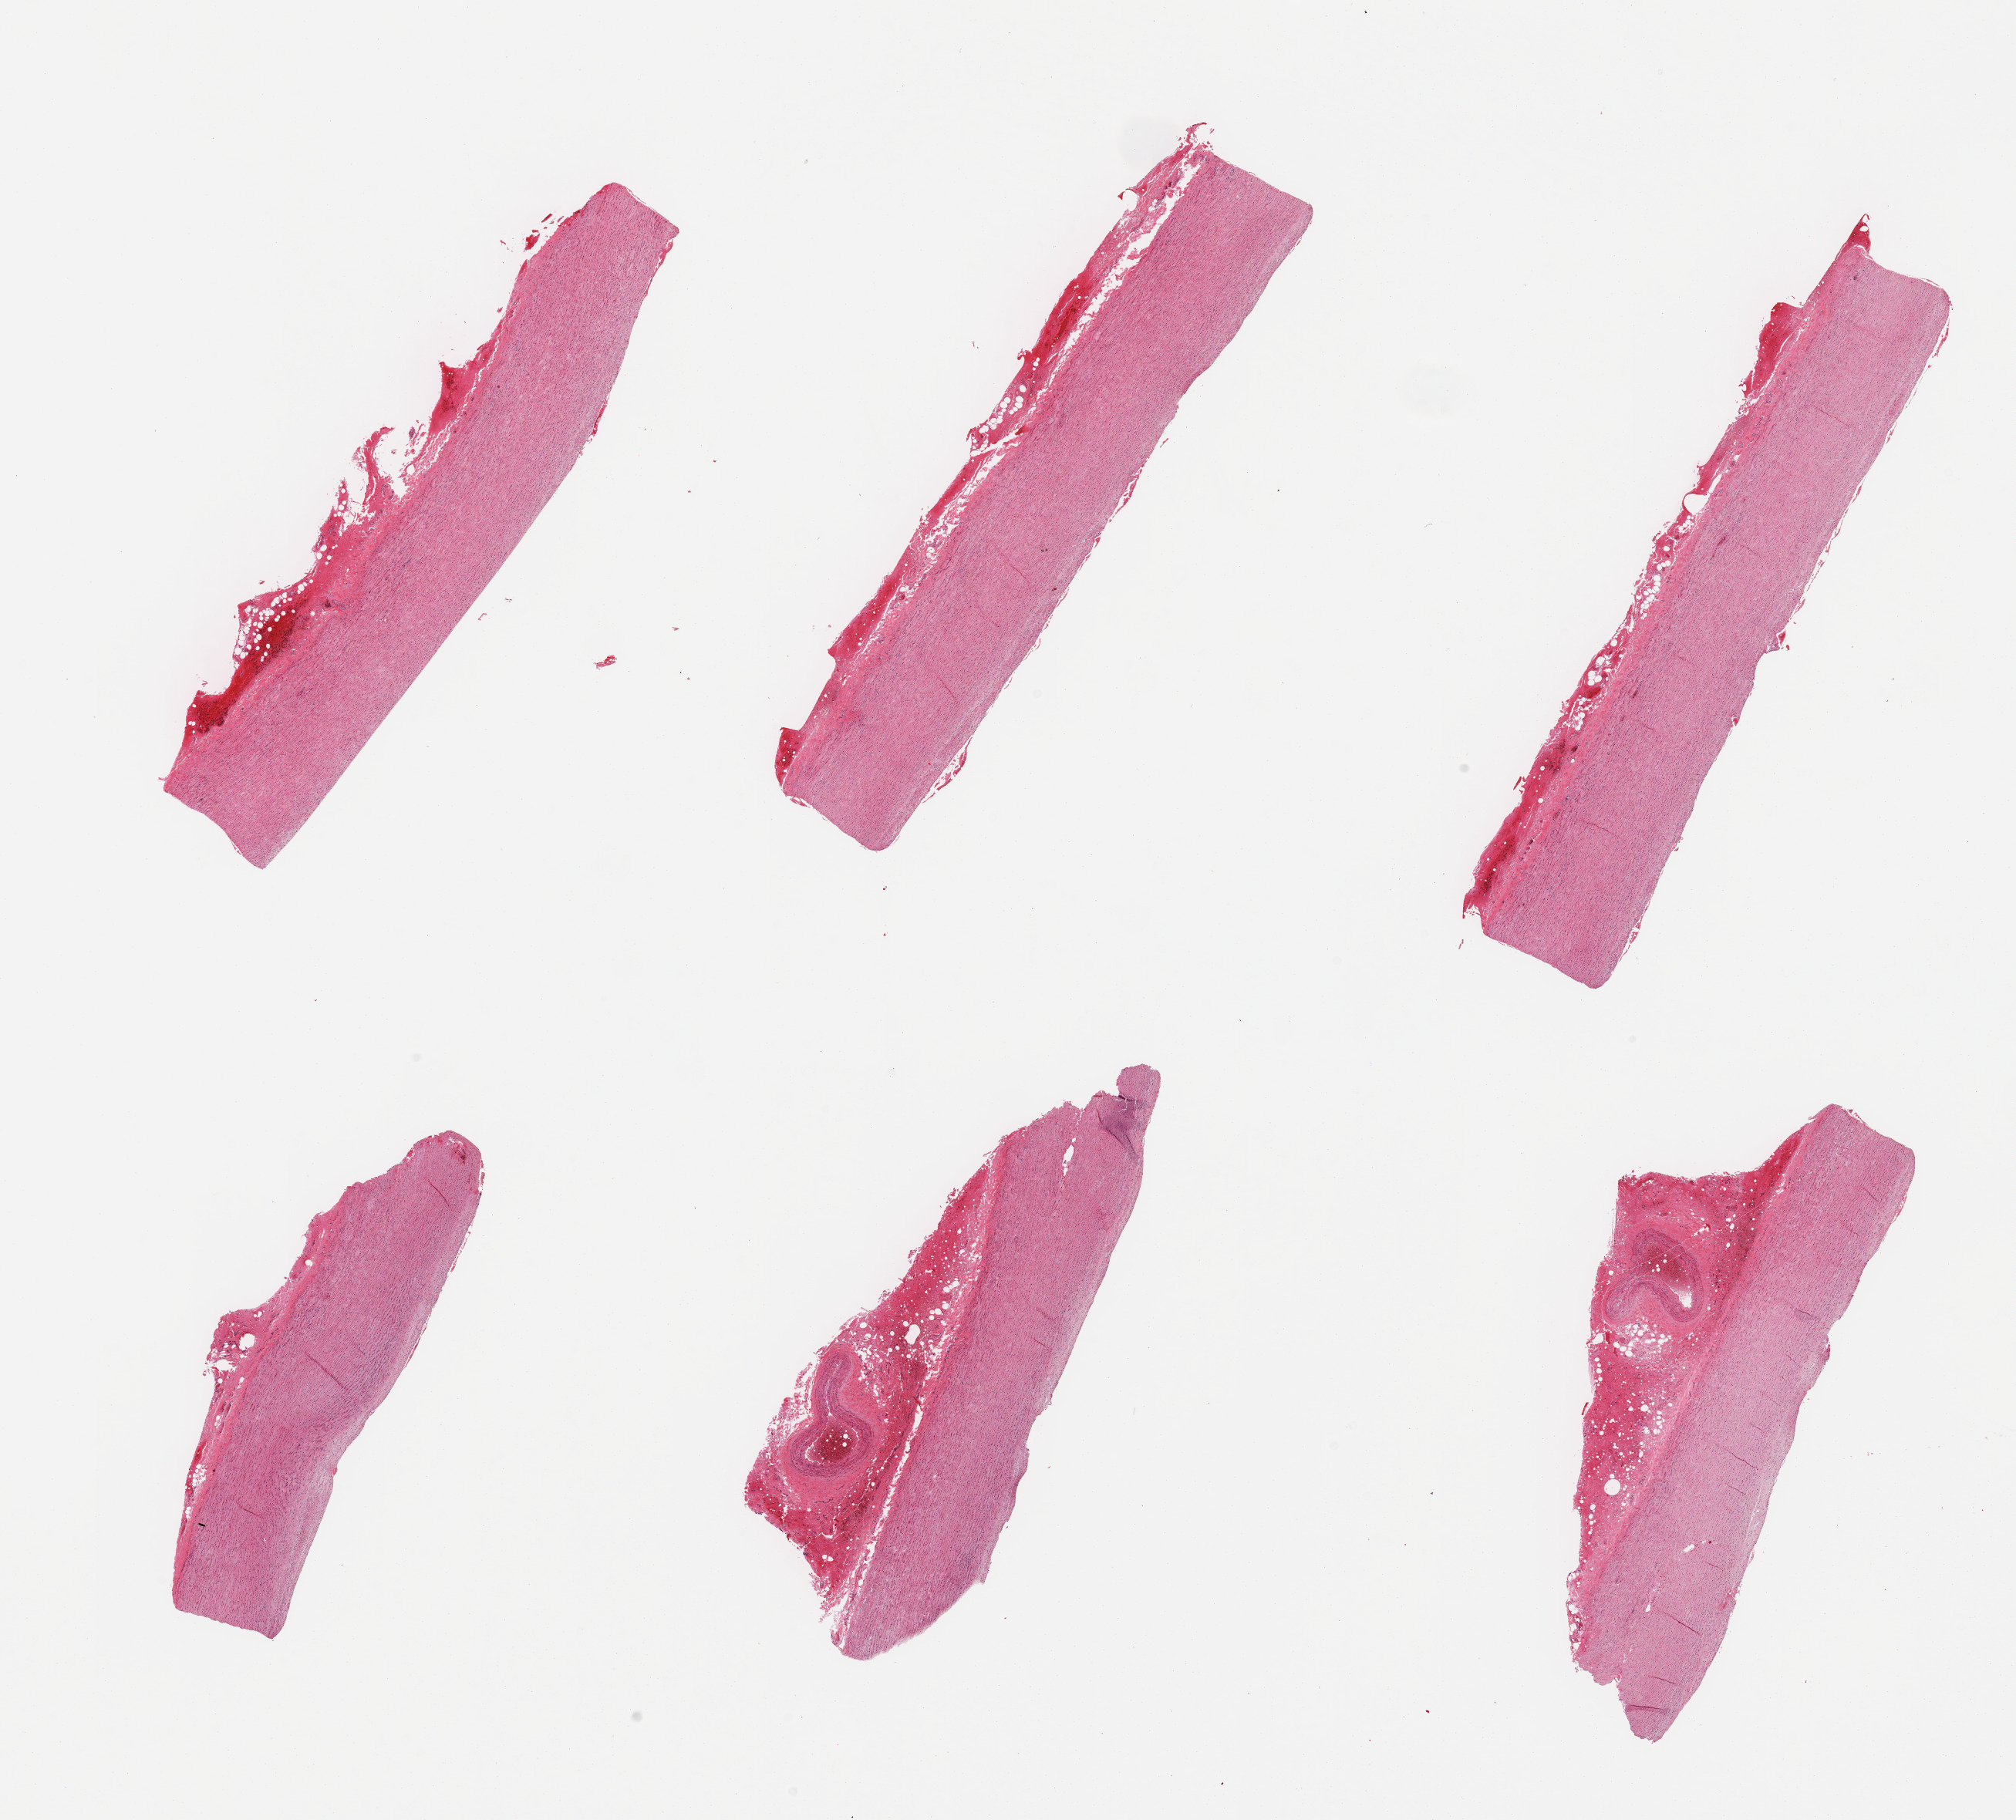
Digitized H&E-stained section — whole scanned area (about 20.7 x 18.7 mm) shown as a low-resolution overview; PAXgene-fixed paraffin-embedded (PFPE) section; section of aorta (target tissue); tissue donor sample.
Review note (as recorded): 6 pieces; 2 pieces have excessive adventitia with artery and fibrofatty stroma; minimal plaque.